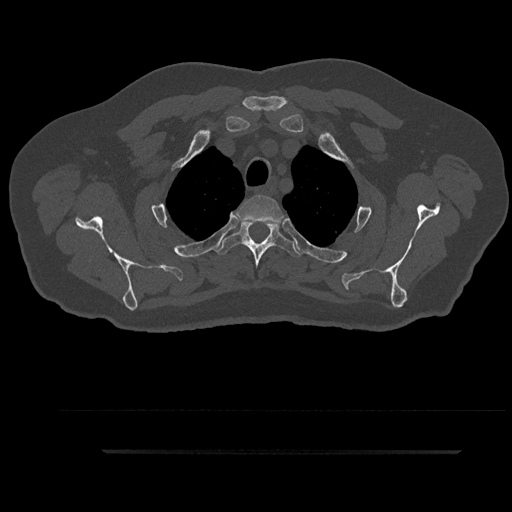
CT including the spine, one axial slice; position 730 of 797 along the scan axis; reconstruction kernel Br40s/3; bone window (W 1800 / L 400 HU); 512 × 512 image matrix, field of view 432 × 432 mm. Patient: male, 63 years. Case-level facts recorded for this patient, not image findings: primary cancer: renal; vertebrae with lytic lesions (as recorded): T8.
Annotated regions visible in this slice (semi-automatic segmentation, software-assisted and operator-edited):
- T2 vertebra: bounding box [x1, y1, x2, y2] px = [236, 194, 284, 223]
- T3 vertebra: [215, 219, 301, 269]